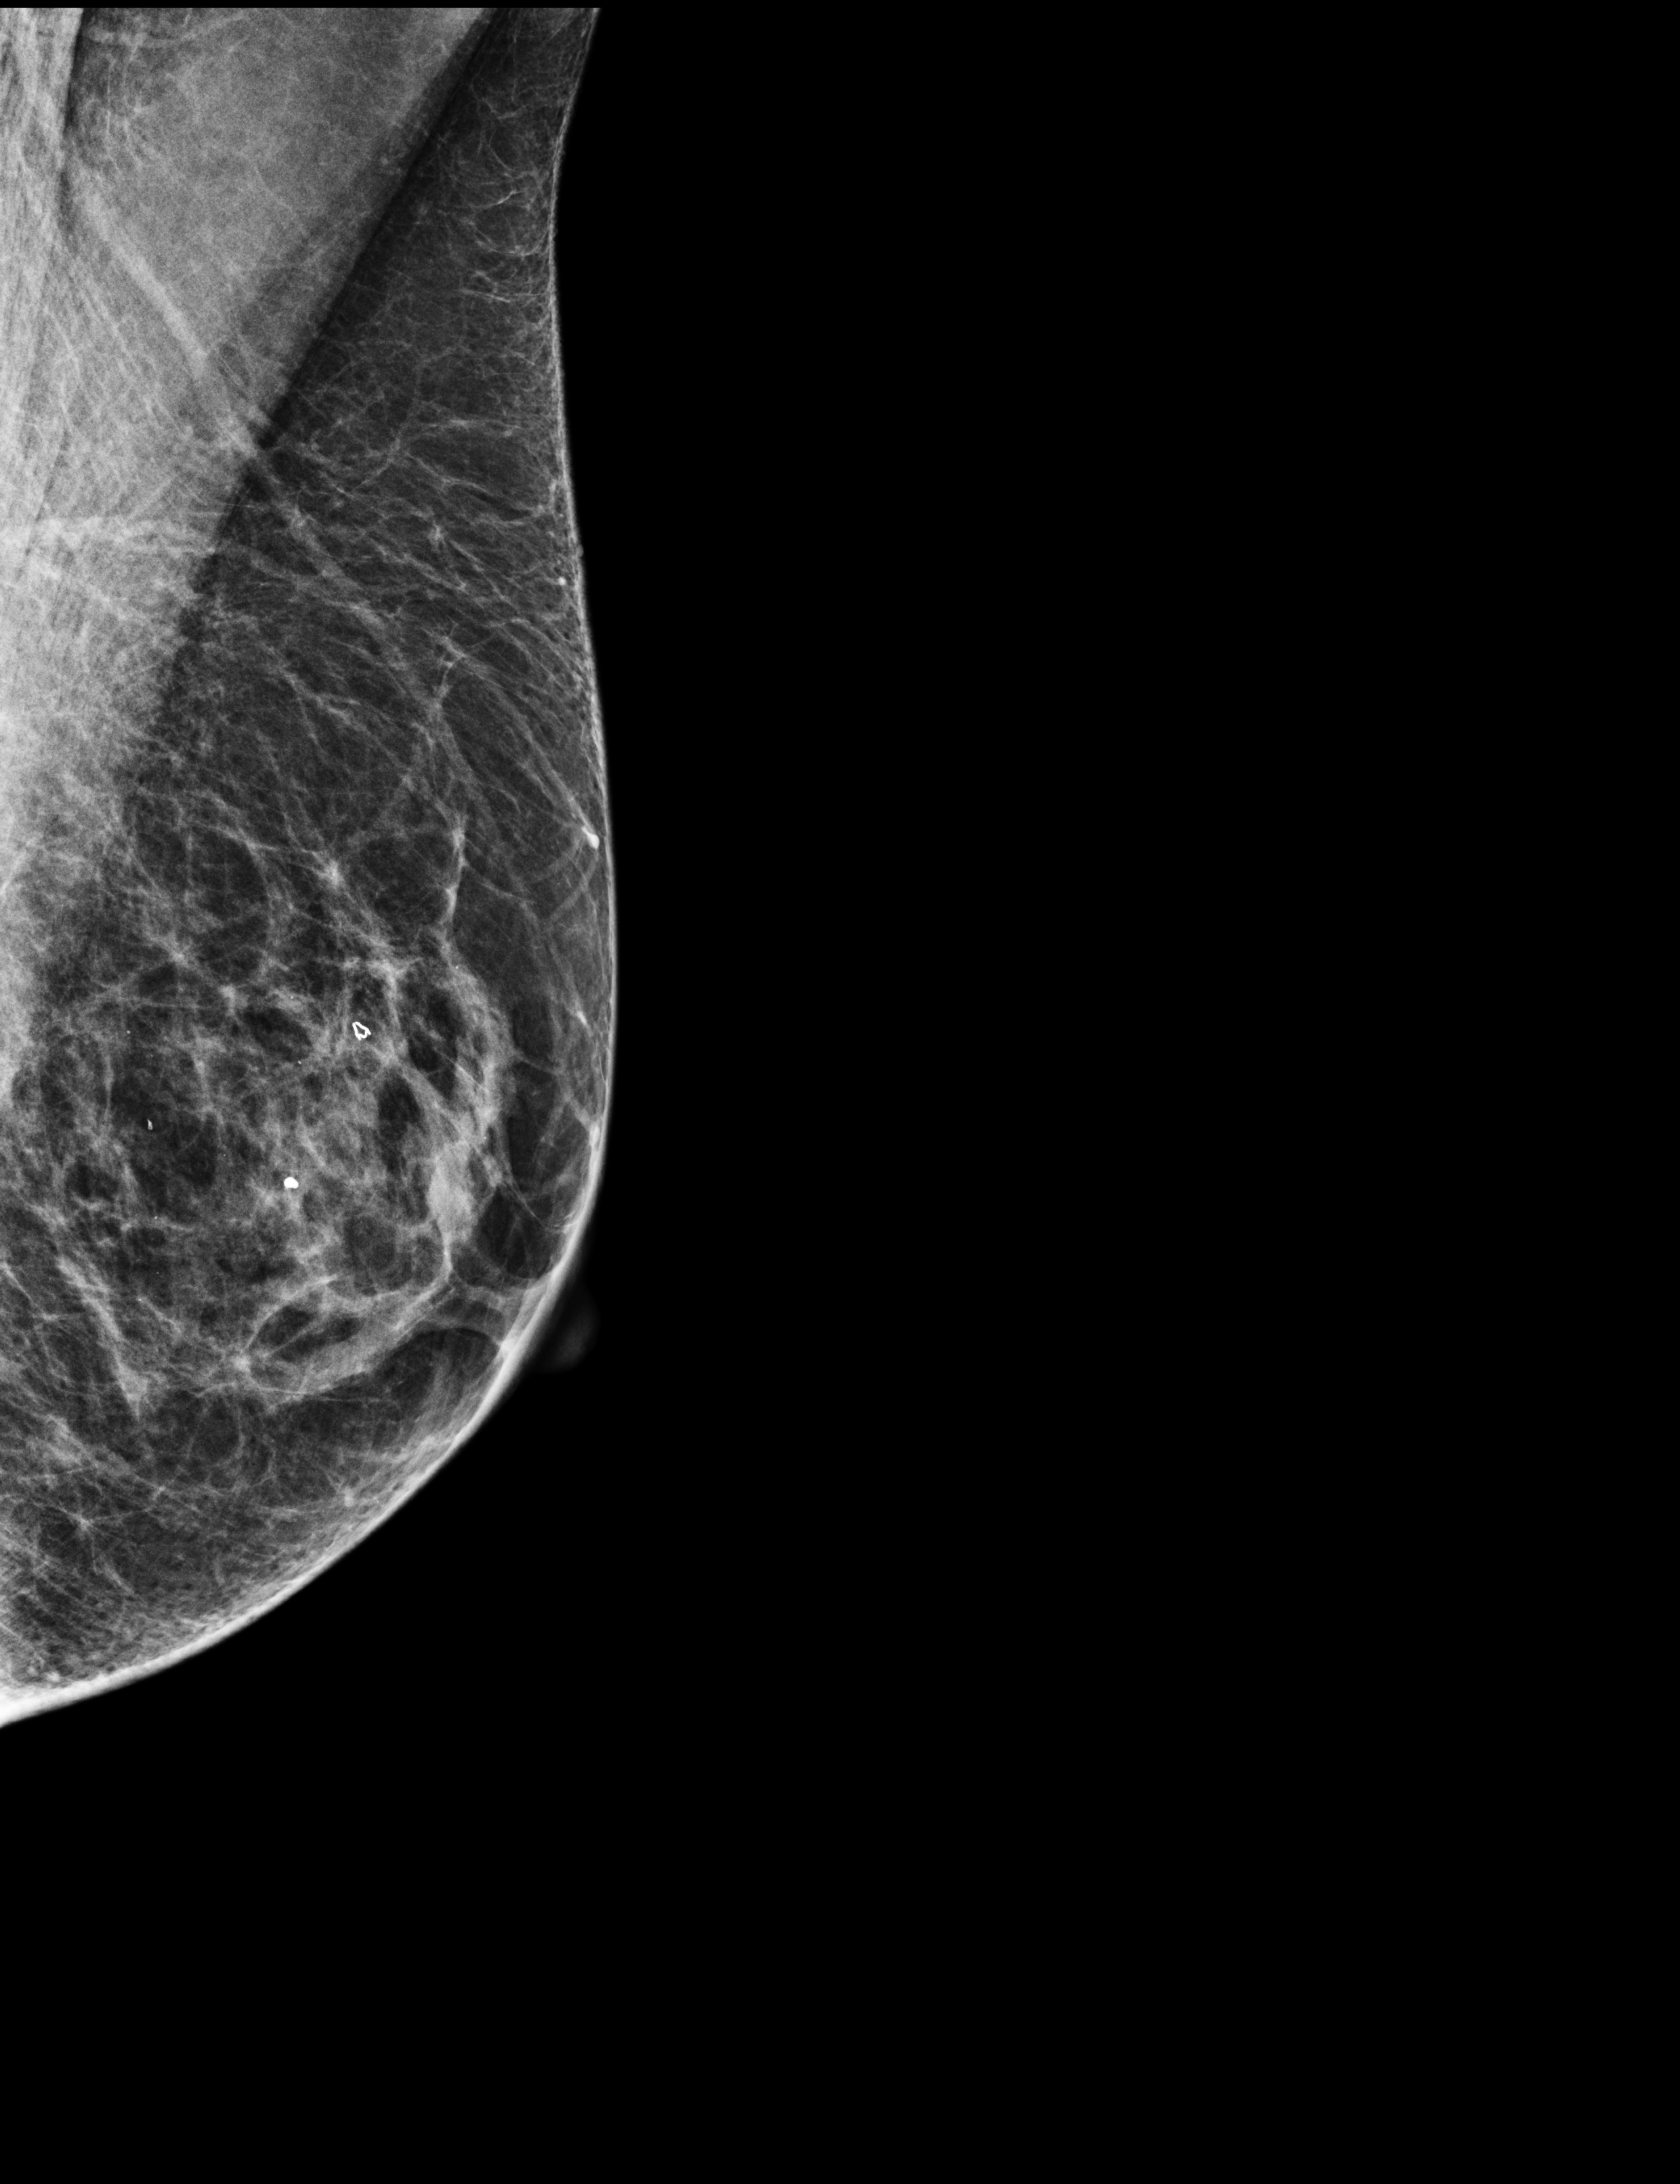
Full-field digital mammogram (FFDM), left breast, MLO view, screening examination, compressed breast thickness 53 mm, system: Selenia Dimensions. Patient: female, 67 years.
- BI-RADS breast density category at the screening exam (both breasts, scale 1–4): 3
- final BI-RADS category for the screening round (tomosynthesis exam, both breasts): category 2
- recall: no recall after this screen